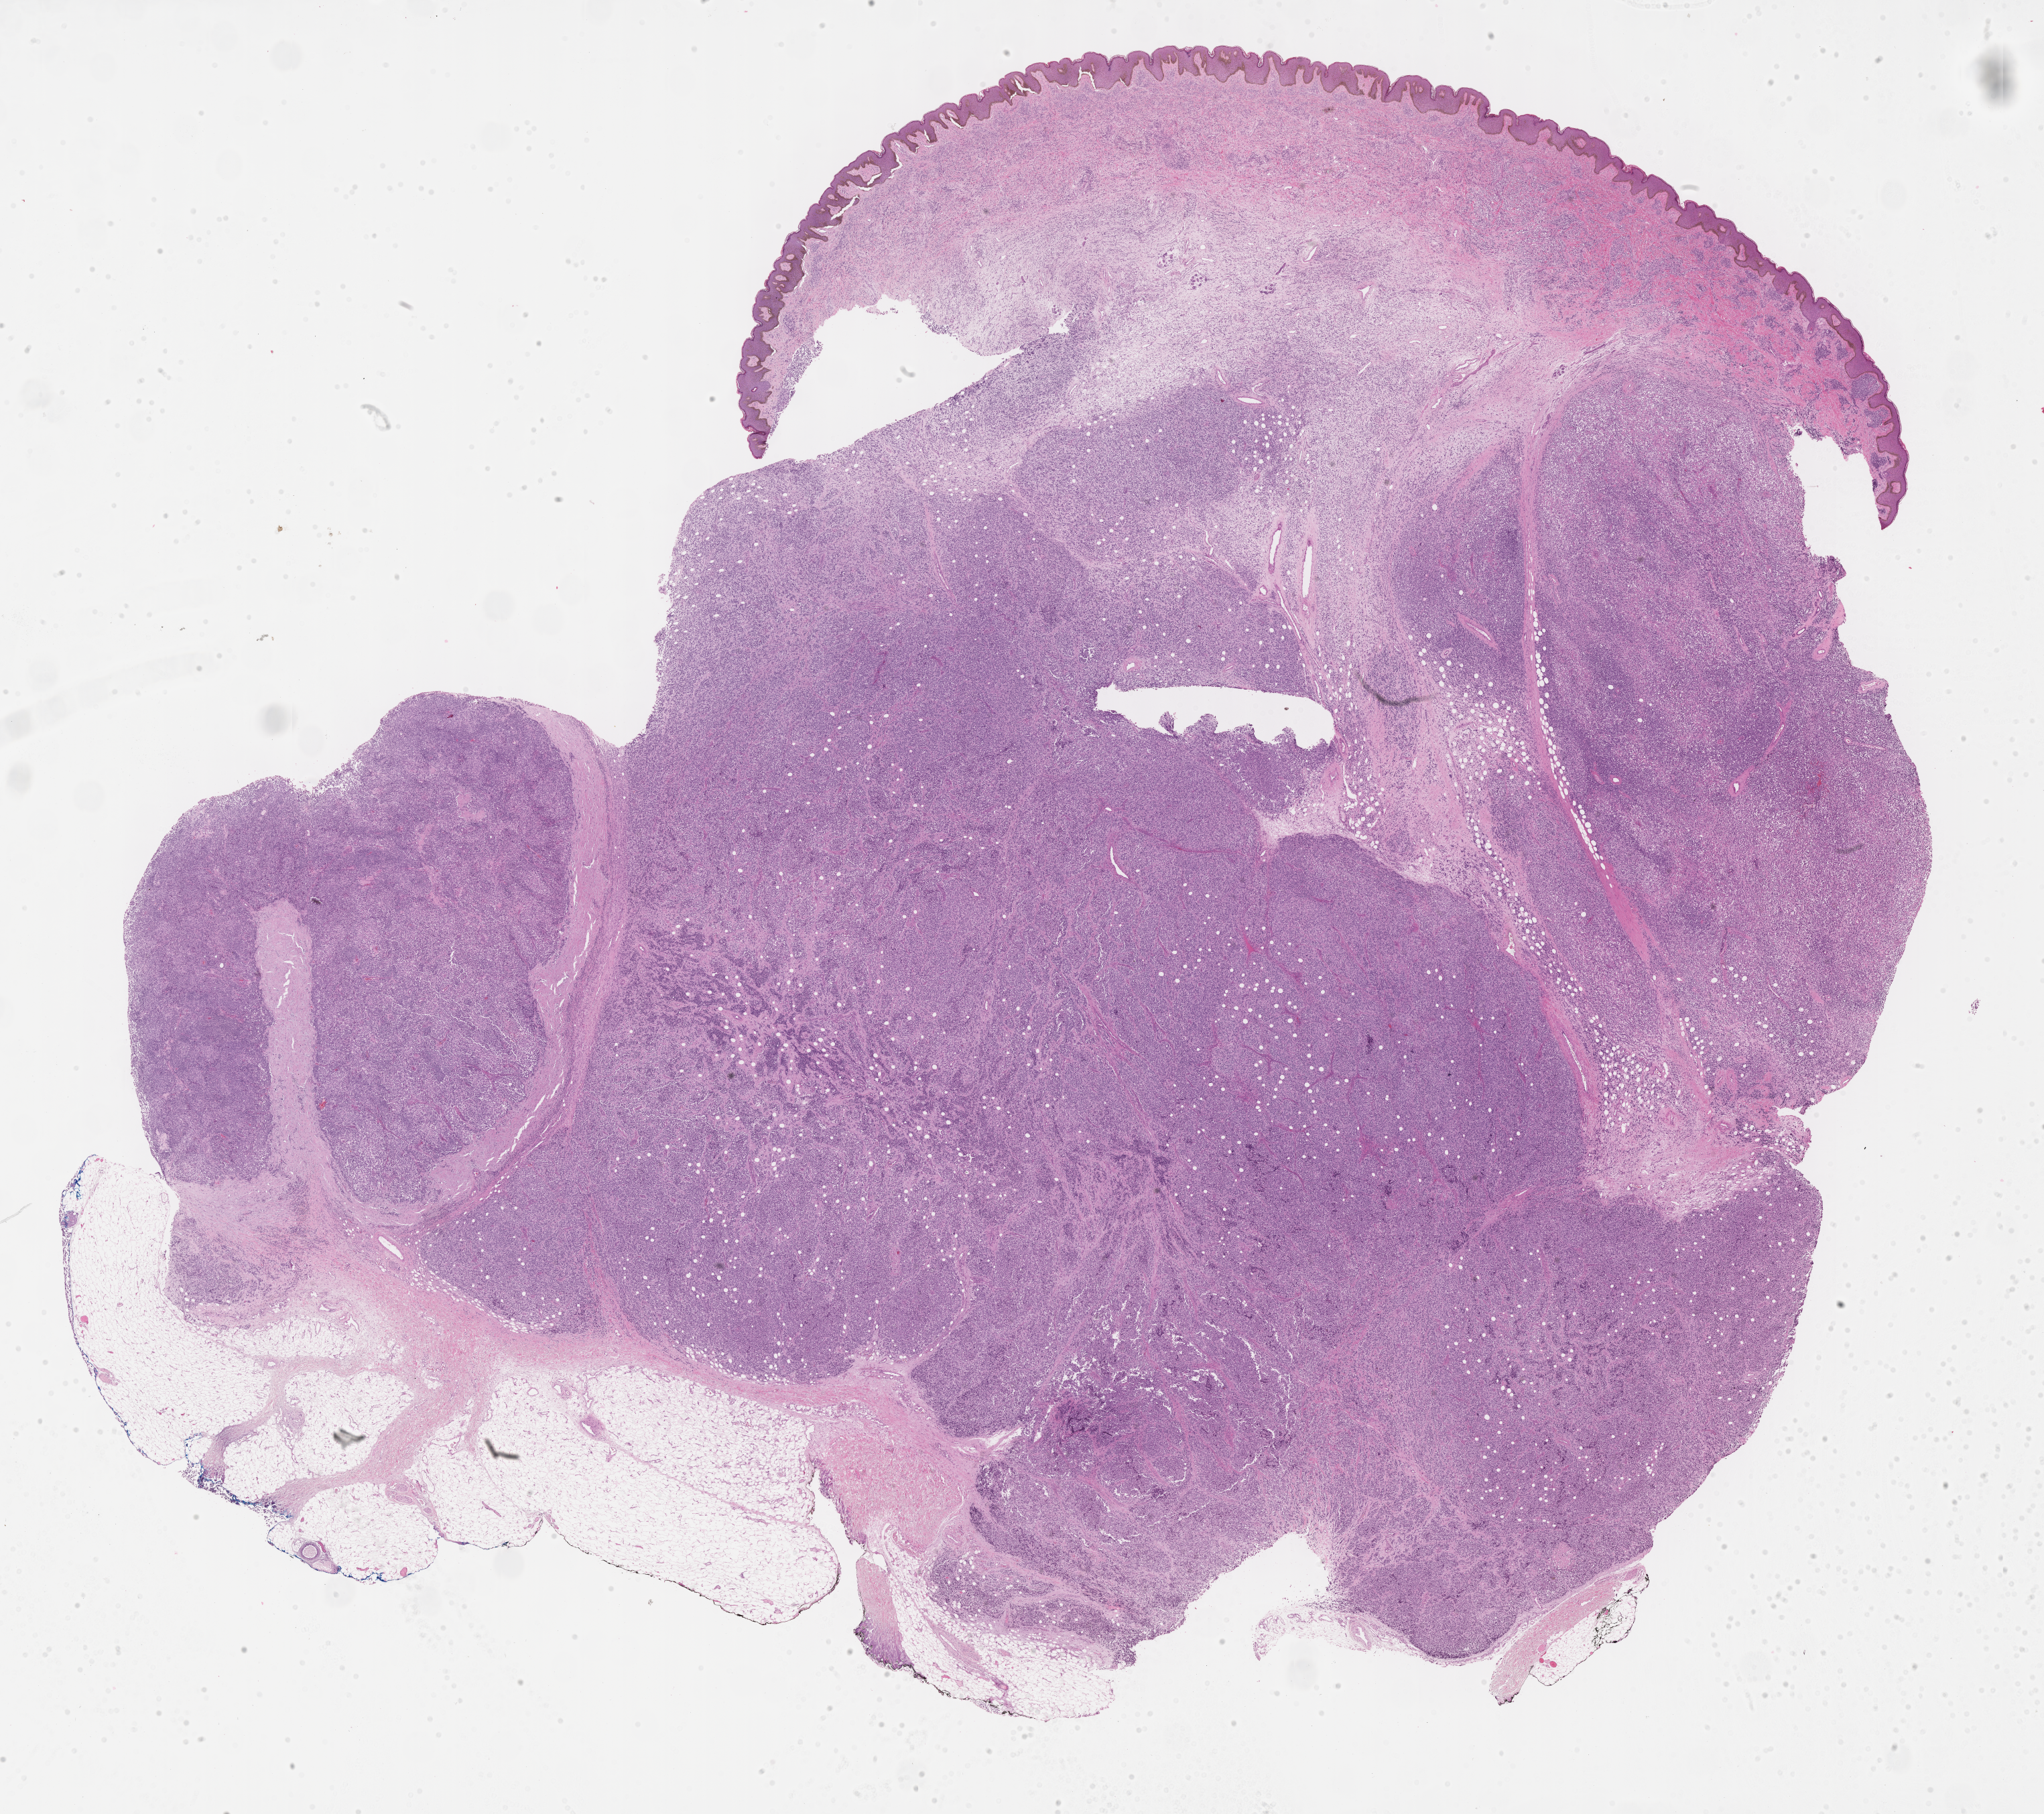
Digitized hematoxylin and eosin (H&E)-stained section of tumor tissue, a low-resolution overview of the entire scanned area, about 24.7 x 21.9 mm. Formalin-fixed, paraffin-embedded (FFPE) tissue. Site: soft tissue, buttock-right. Male patient, age at diagnosis 0.9 years.
Stage (as recorded): 4. Diagnosis: rhabdomyosarcoma; histological classification: alveolar rhabdomyosarcoma. Metastatic status at presentation (as recorded): metastatic (confirmed).